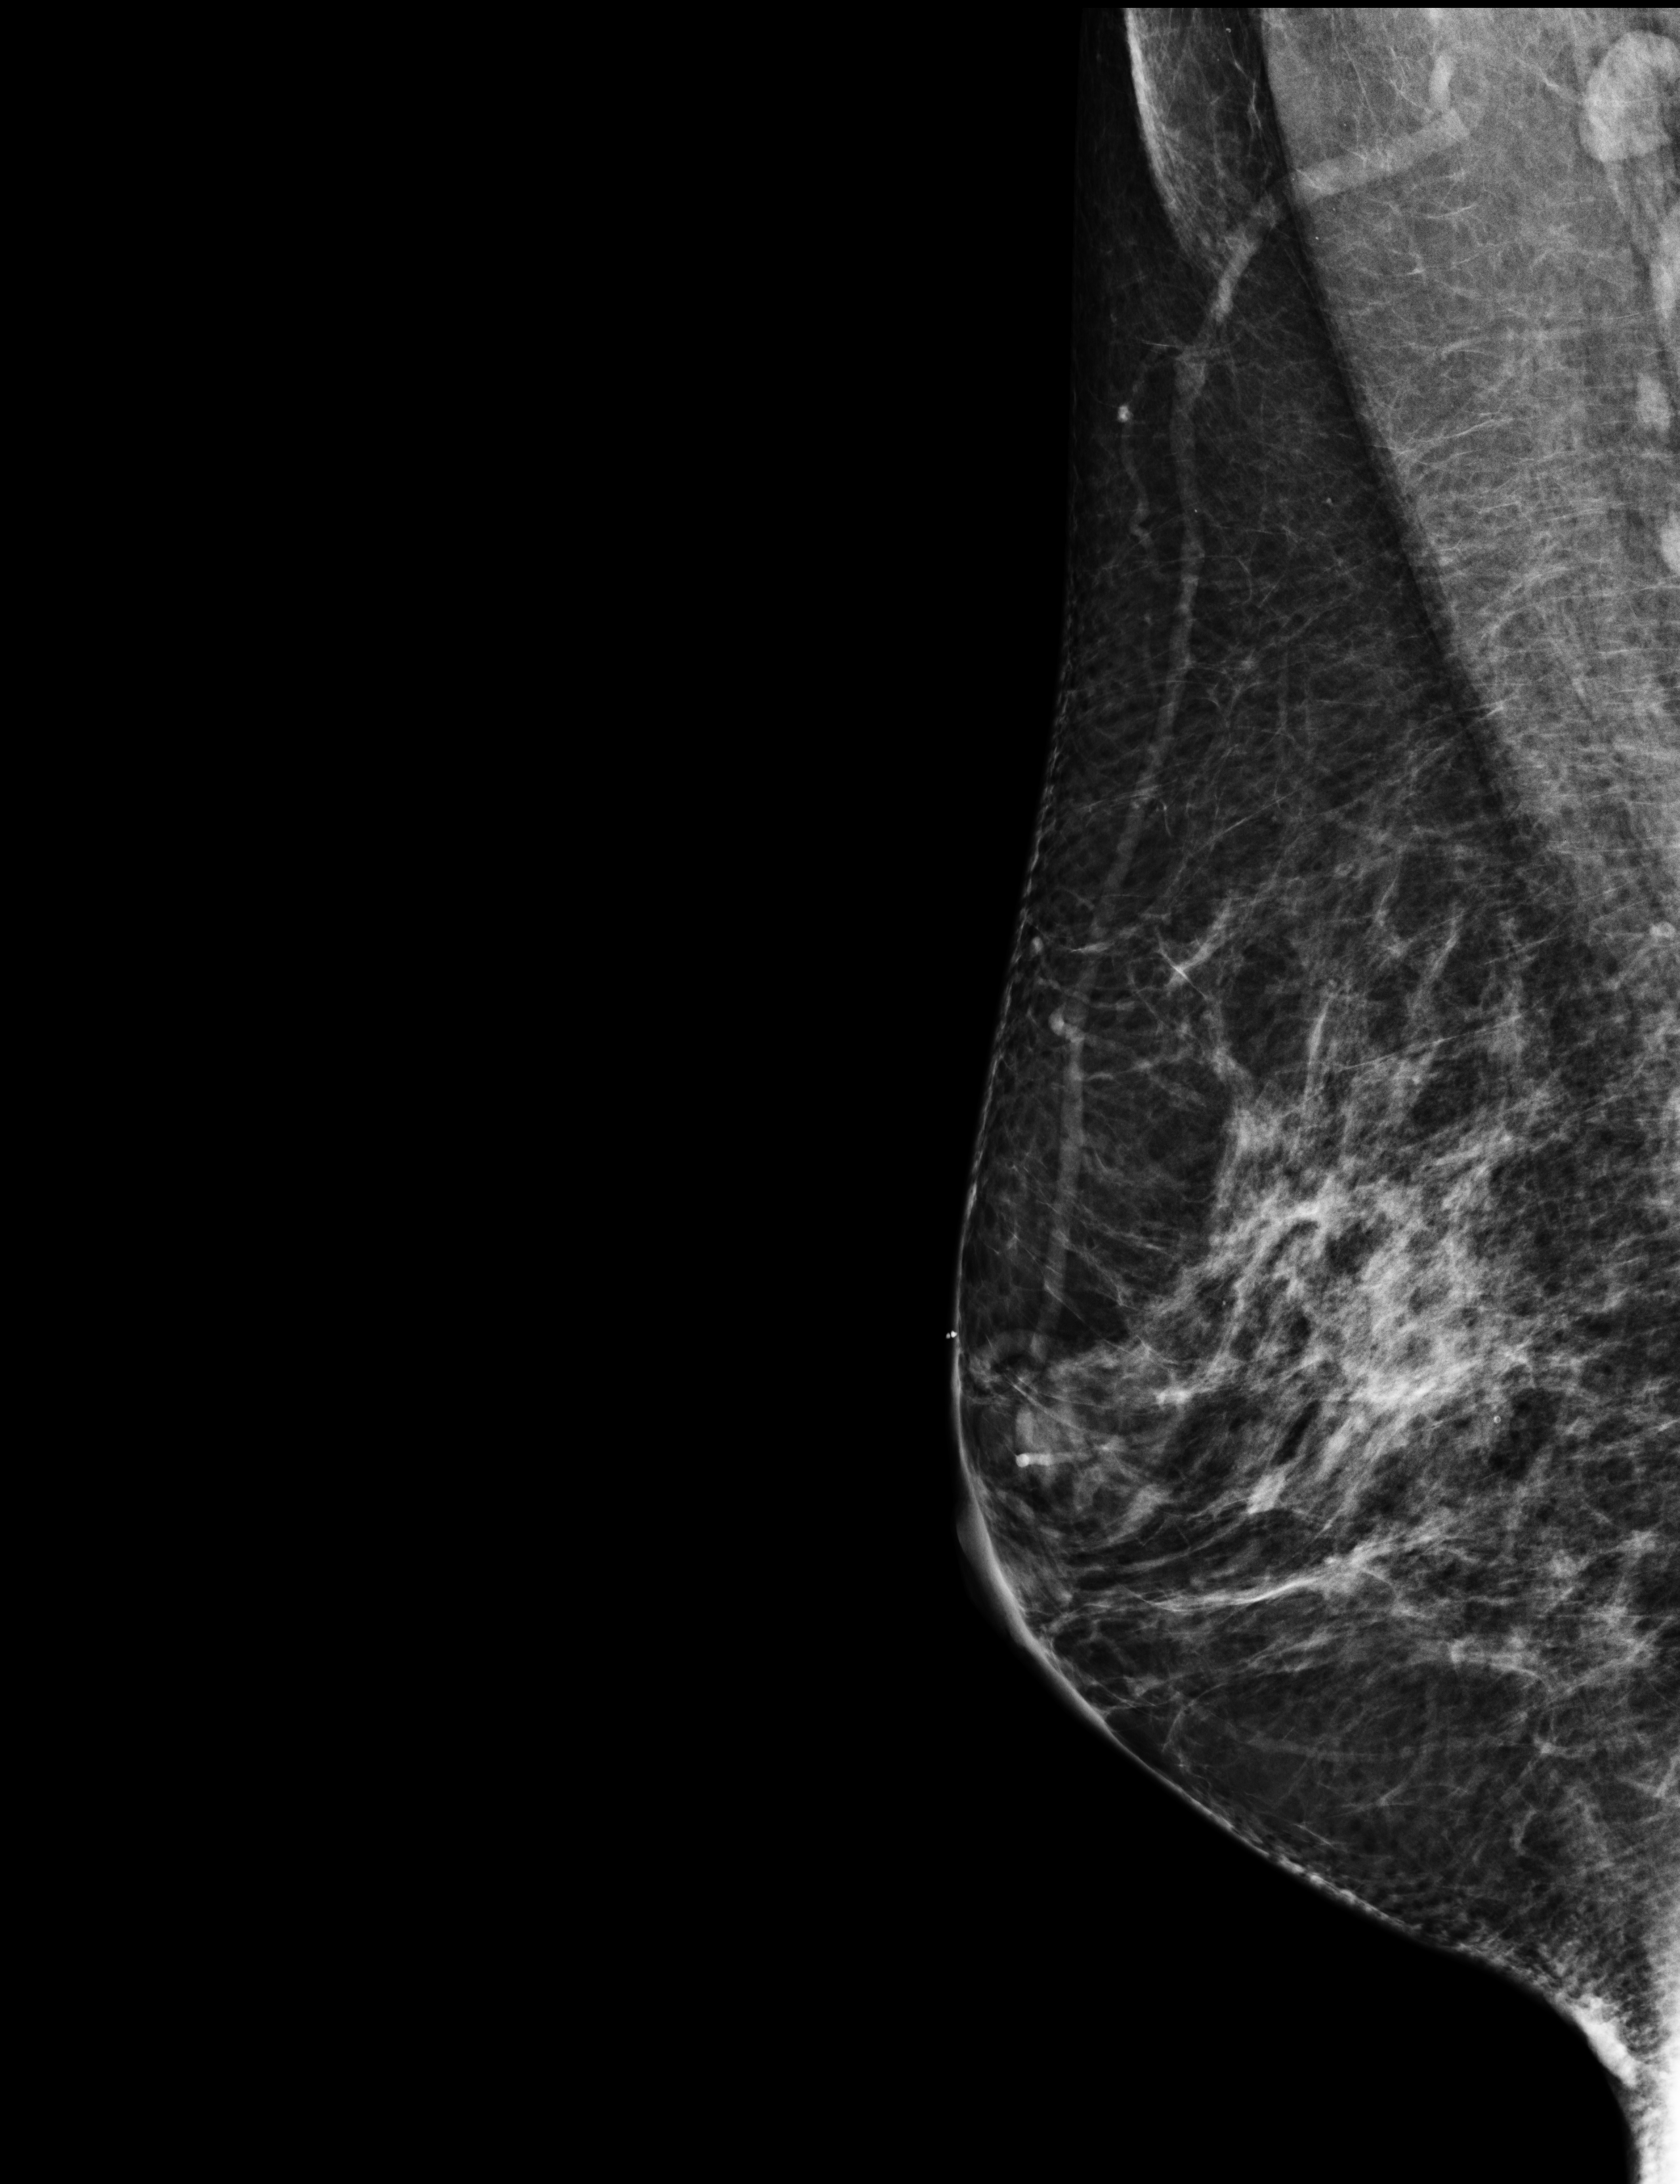
Annual screening mammography examination; compressed breast thickness 74 mm; system: Selenia Dimensions.
Image type: full-field digital mammogram. Breast: right. Projection: medio-lateral oblique projection.